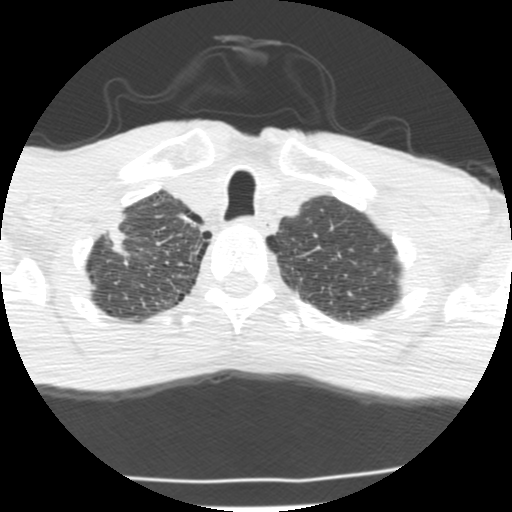
Low-dose screening chest CT, one axial slice. Slice 188 of 214 in the series (ordered by position). Lung window (W 1500 / L -600 HU). 2.5 mm slice thickness. 512 × 512 image matrix, field of view 283 × 283 mm.
Outlined on this slice (expert manual segmentation):
- lesion 1 (tumor, upper lobe of right lung): bounding box [x1, y1, x2, y2] px = [105, 214, 130, 258]